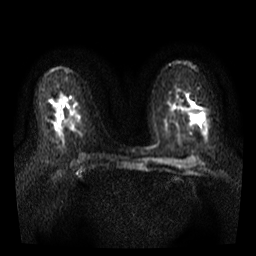
Breast MRI, one axial slice; slice 19 of 35 in the series (ordered by position); diffusion-weighted series; image 2 of 4 stored at this slice position (different b-values; order by instance number); 3 T; 5 mm slice thickness; 256 × 256 image matrix. Female patient.
Outlined on this slice (expert manual segmentation):
- tumour on diffusion-weighted imaging: box from (x=191, y=110) to (x=204, y=122) px